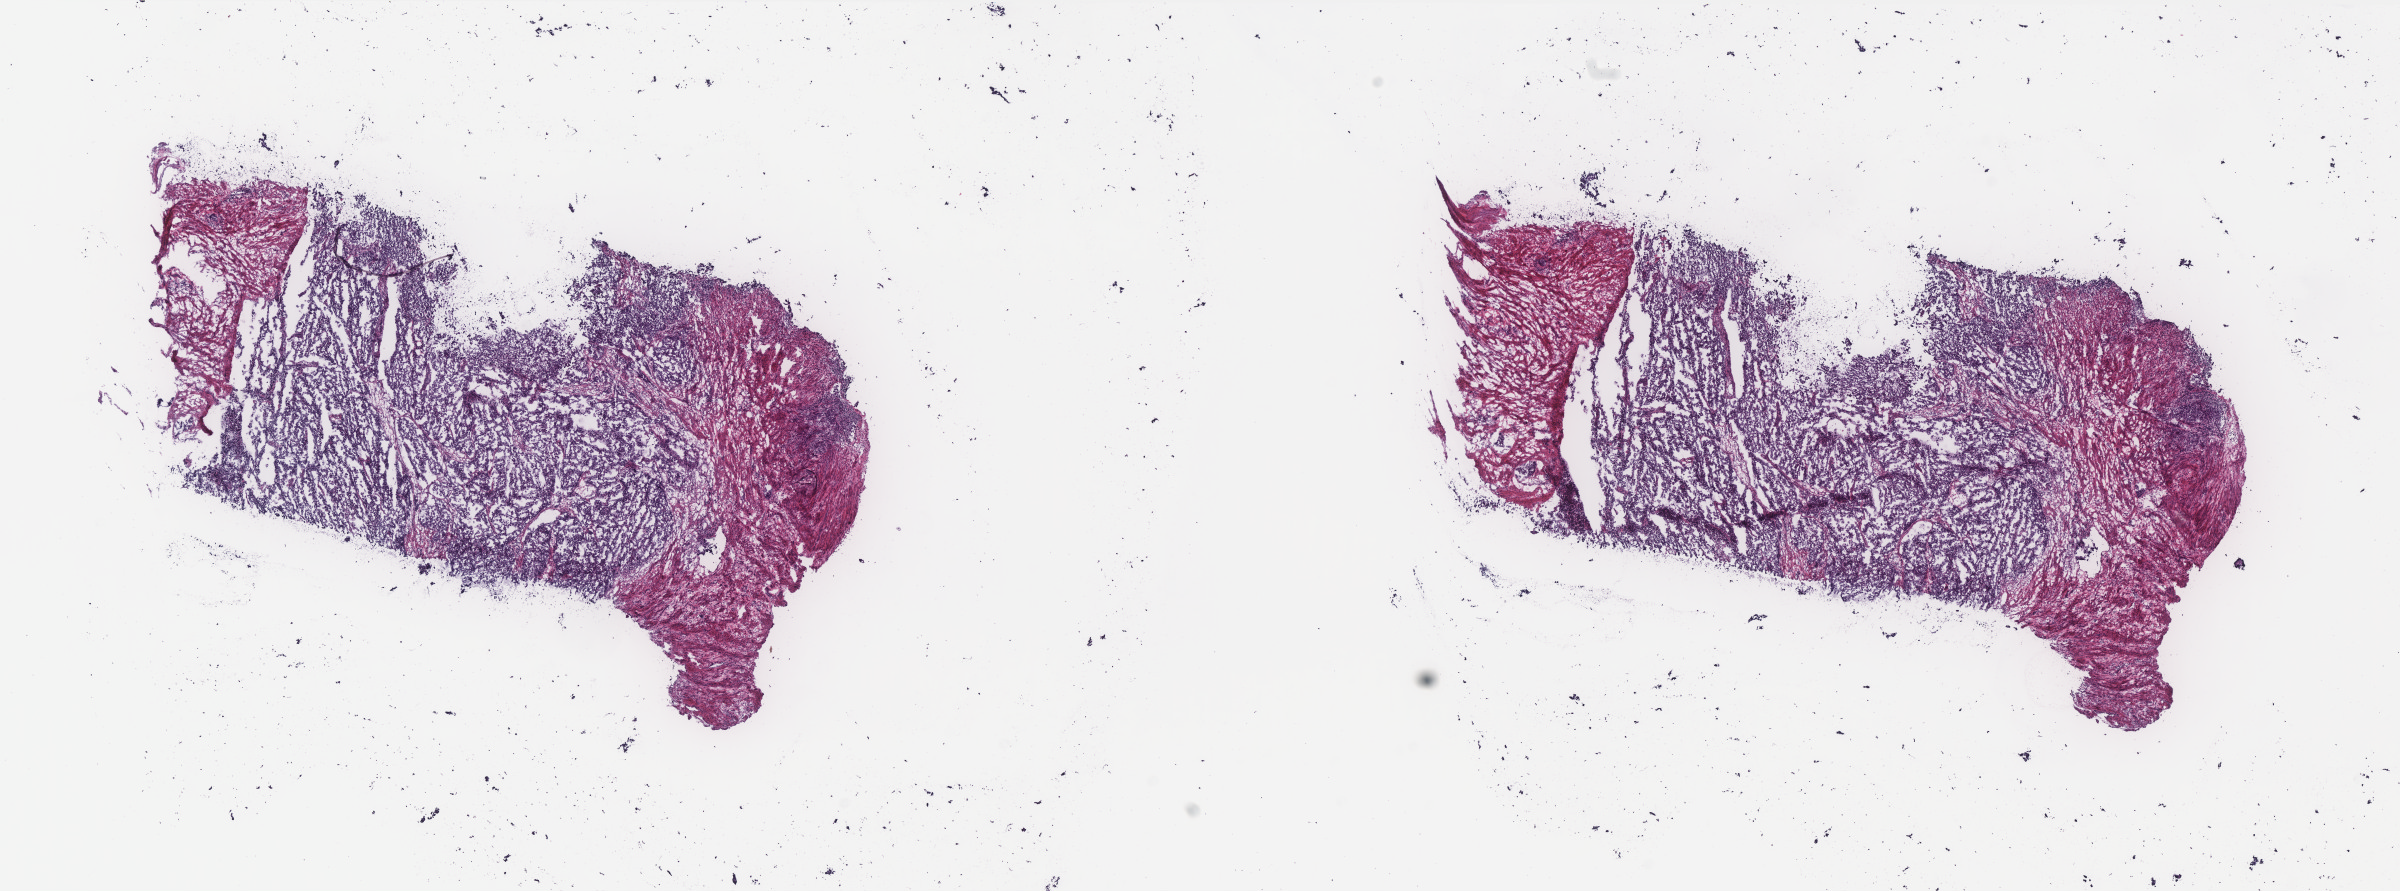
Digitized H&E-stained tissue section (whole slide) — low-resolution overview of the scanned area, about 19.2 x 7.1 mm (acquisition: 40x scan). Frozen section. Uterus, primary tumour sample. Female patient; age at initial diagnosis 70 years. Histologic grade: G3 (poorly differentiated). Pathologist review of this section (percent, as recorded): tumour cells 70%, tumour nuclei 70%, normal cells 0%, stromal cells 30%, necrosis 0%. Inflammatory infiltration, as recorded: lymphocyte infiltration 30%, monocyte infiltration 5%, neutrophil infiltration 3%.
Diagnosis: Serous cystadenocarcinoma, NOS (endometrium). FIGO stage: IIIC1.